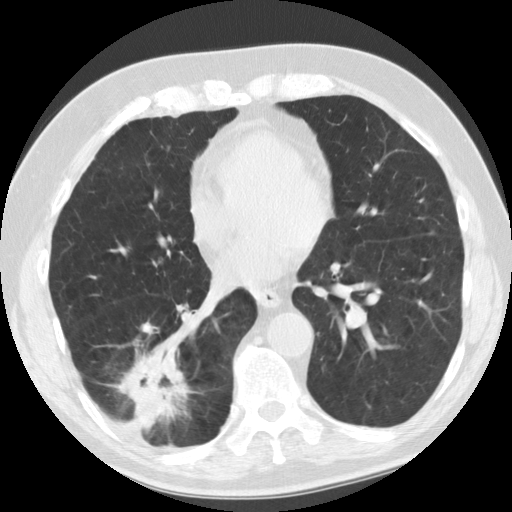
Axial slice from a low-dose chest CT screening exam, baseline annual screen, lung window (W 1500 / L -600 HU). Male, age 69 years at enrolment.
• Expert-annotated lung lesion, bounding box [x1, y1, x2, y2] px = [110, 332, 196, 441].
• The screening reader recorded 2 non-calcified nodules or masses ≥4 mm on this exam (right lower lobe, right lower lobe); which of them this box marks is not recorded.
• Official screen result: positive, change unspecified: nodule(s) >= 4 mm or enlarging nodule(s), mass(es), or other non-specific abnormalities suspicious for lung cancer.
• Lung cancer was diagnosed 40 days after this screen: adenocarcinoma, NOS, right lower lobe, stage IIB (AJCC 6th edition), 45 mm at pathology.